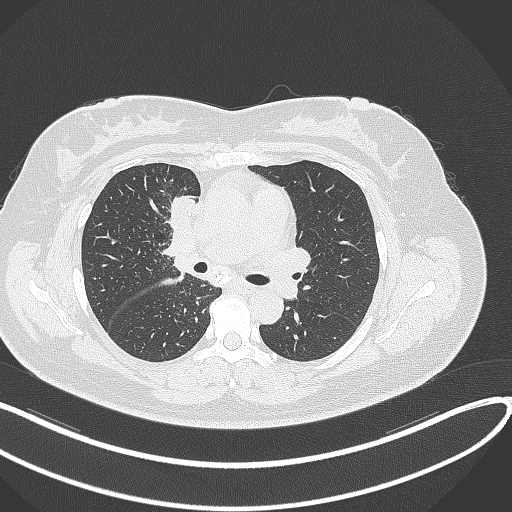
Chest CT, one axial slice. Slice 162 of 303 in the series (ordered by position). Lung window (W 1500 / L -600 HU). 512 × 512 image matrix. Patient: female, 46 years. From the clinical record (not read from this slice): clinical TNM (as recorded): T2a N1 M0.
Outlined on this slice (bounding box drawn by a radiologist):
- lung tumour (recorded histology: adenocarcinoma): bounding box <161,191,198,226> (left, top, right, bottom; pixels)